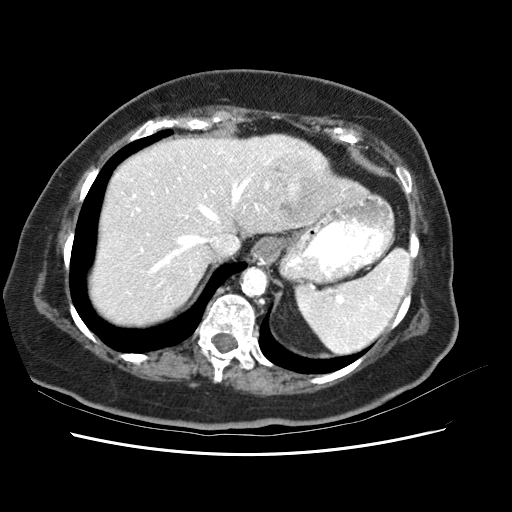
Contrast-enhanced abdominal CT (liver protocol), one axial slice. Position 49 of 62 along the scan axis. Reconstruction kernel STANDARD. 120 kVp. Soft-tissue window (W 400 / L 40 HU). 2.5 mm slice thickness. 512 × 512 image matrix. From the clinical record (not read from this slice): diagnosis: hepatocellular carcinoma (patient treated with transarterial chemoembolisation; whether this scan precedes or follows treatment is not stated here); TNM stage (as recorded): Stage-I.
Outlined on this slice (semi-automatic segmentation, software-assisted and operator-edited):
- liver parenchyma outside the tumour (the mass and vessels are separate outlines, so this box may not span the whole liver): box from (x=104, y=136) to (x=334, y=312) px
- mass: (x=262, y=148)–(x=329, y=219)
- liver vessels: (x=125, y=156)–(x=269, y=290)